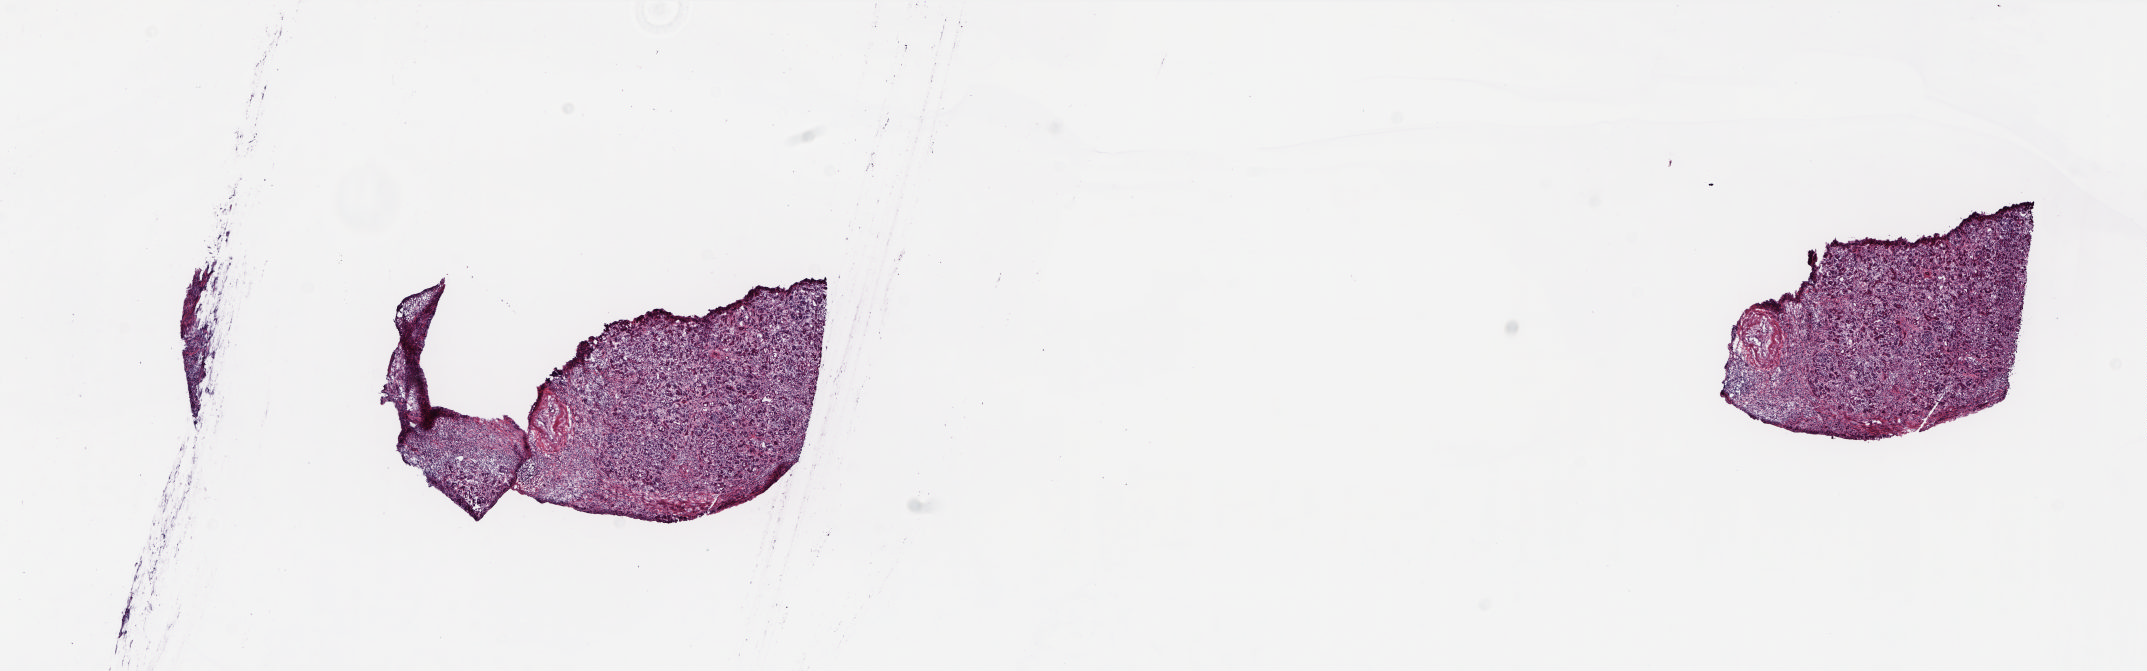
Whole-slide histology image, H&E — a low-resolution overview of the entire scanned area, about 17.3 x 5.4 mm, frozen section from the top of the tissue portion, sample: solid tissue normal (non-tumour tissue), pancreas. Male, age 50 years at initial diagnosis. Pathologist review of this section (percent, as recorded): tumour cells 0%, tumour nuclei 0%, normal cells 100%, stromal cells 0%, necrosis 0%. Inflammatory infiltration, as recorded: lymphocyte infiltration 8%, monocyte infiltration 3%, neutrophil infiltration 0%.
This section: solid tissue normal sample (biorepository sample class). Patient diagnosis: Infiltrating duct carcinoma, NOS (body of pancreas).